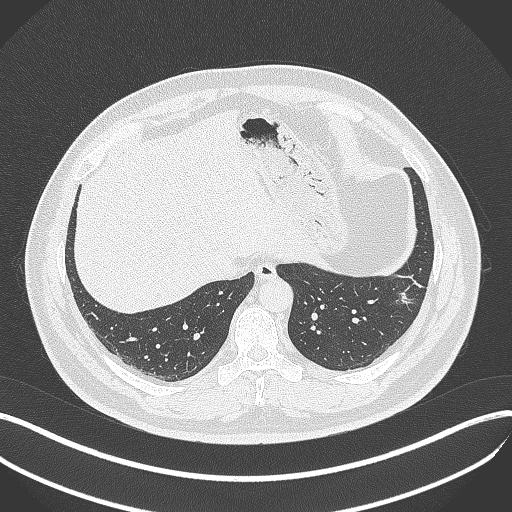
Chest CT, one axial slice. Slice 105 of 429 in the series (ordered by position). 120 kVp. Lung window (W 1500 / L -600 HU). 512 × 512 image matrix. Patient: male, 39 years. From the clinical record (not read from this slice): clinical TNM (as recorded): T2a N0 M0; histopathological grade: G2-3.
Annotated regions visible in this slice (bounding box drawn by a radiologist):
- lung tumour (recorded histology: adenocarcinoma): bounding box (x1, y1, x2, y2) in pixels: (394, 281, 423, 318)